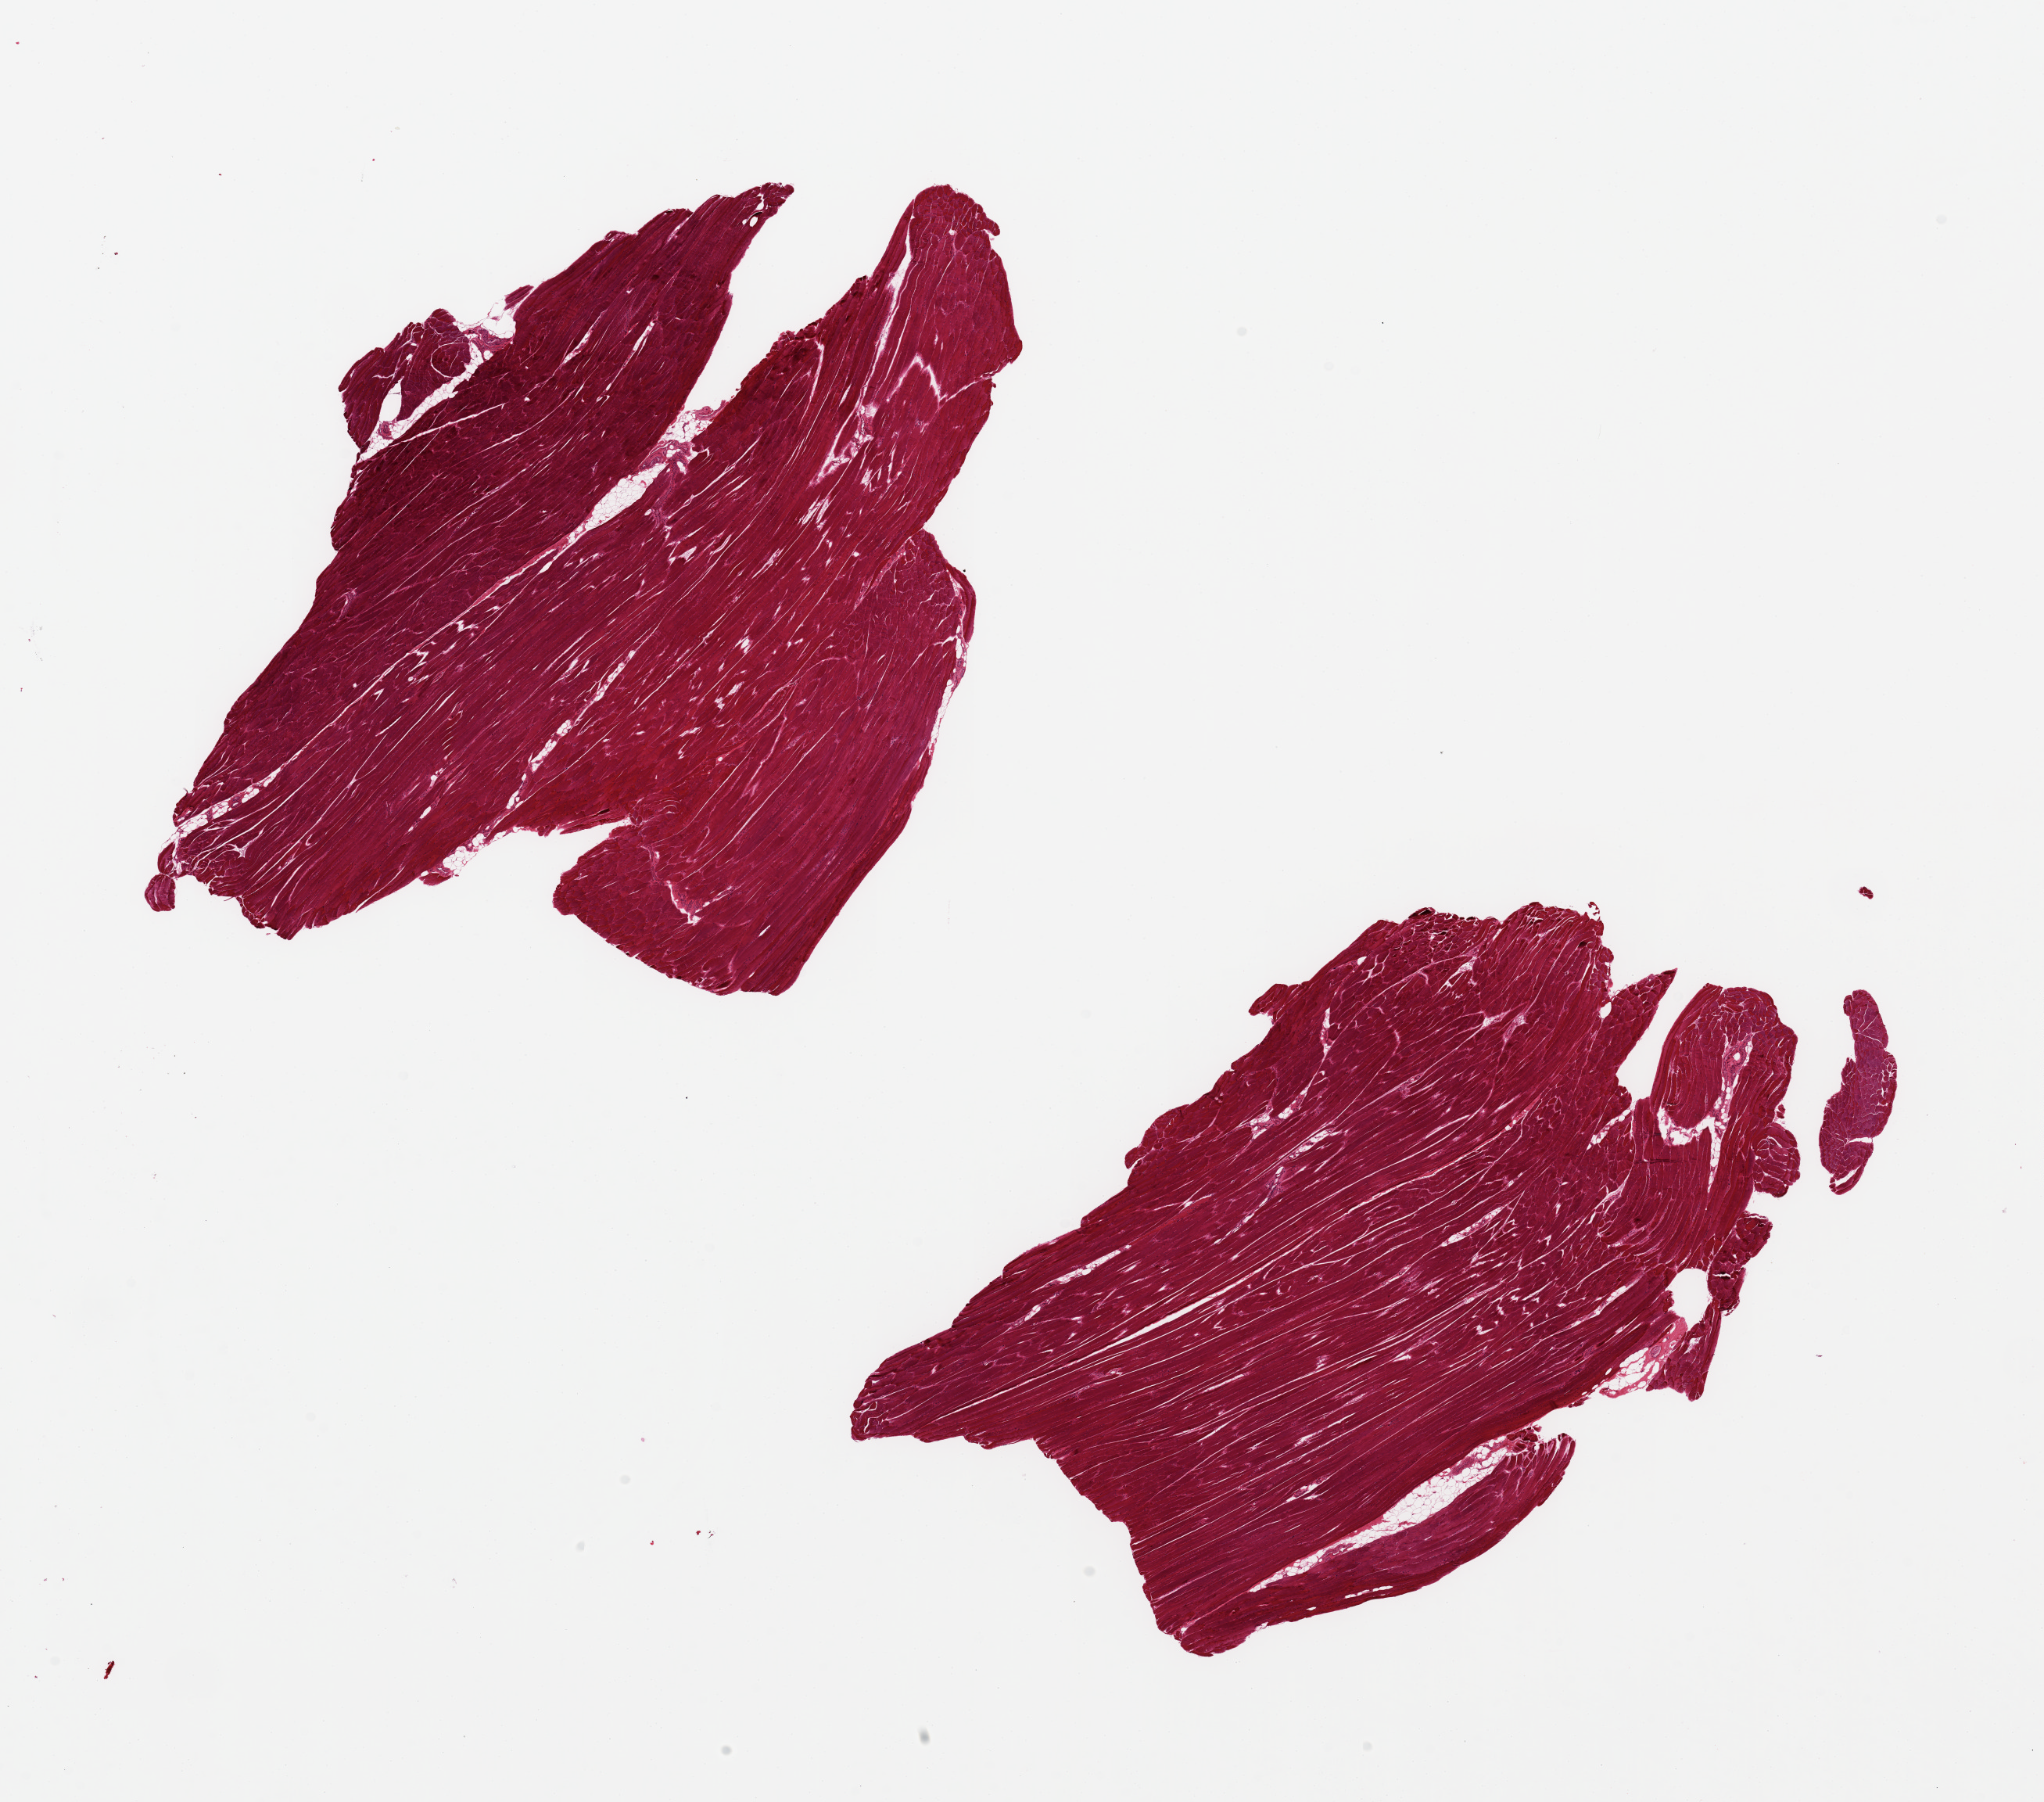
H&E whole-slide image — whole scanned area (about 20.7 x 18.2 mm) shown as a low-resolution overview, PAXgene-fixed paraffin-embedded (PFPE) section, sampled site (target tissue): skeletal muscle, donor tissue sample.
Pathologist's review note for this sample: 2 pieces, ~10x6mm, Minimal interstitial fat (<5%).